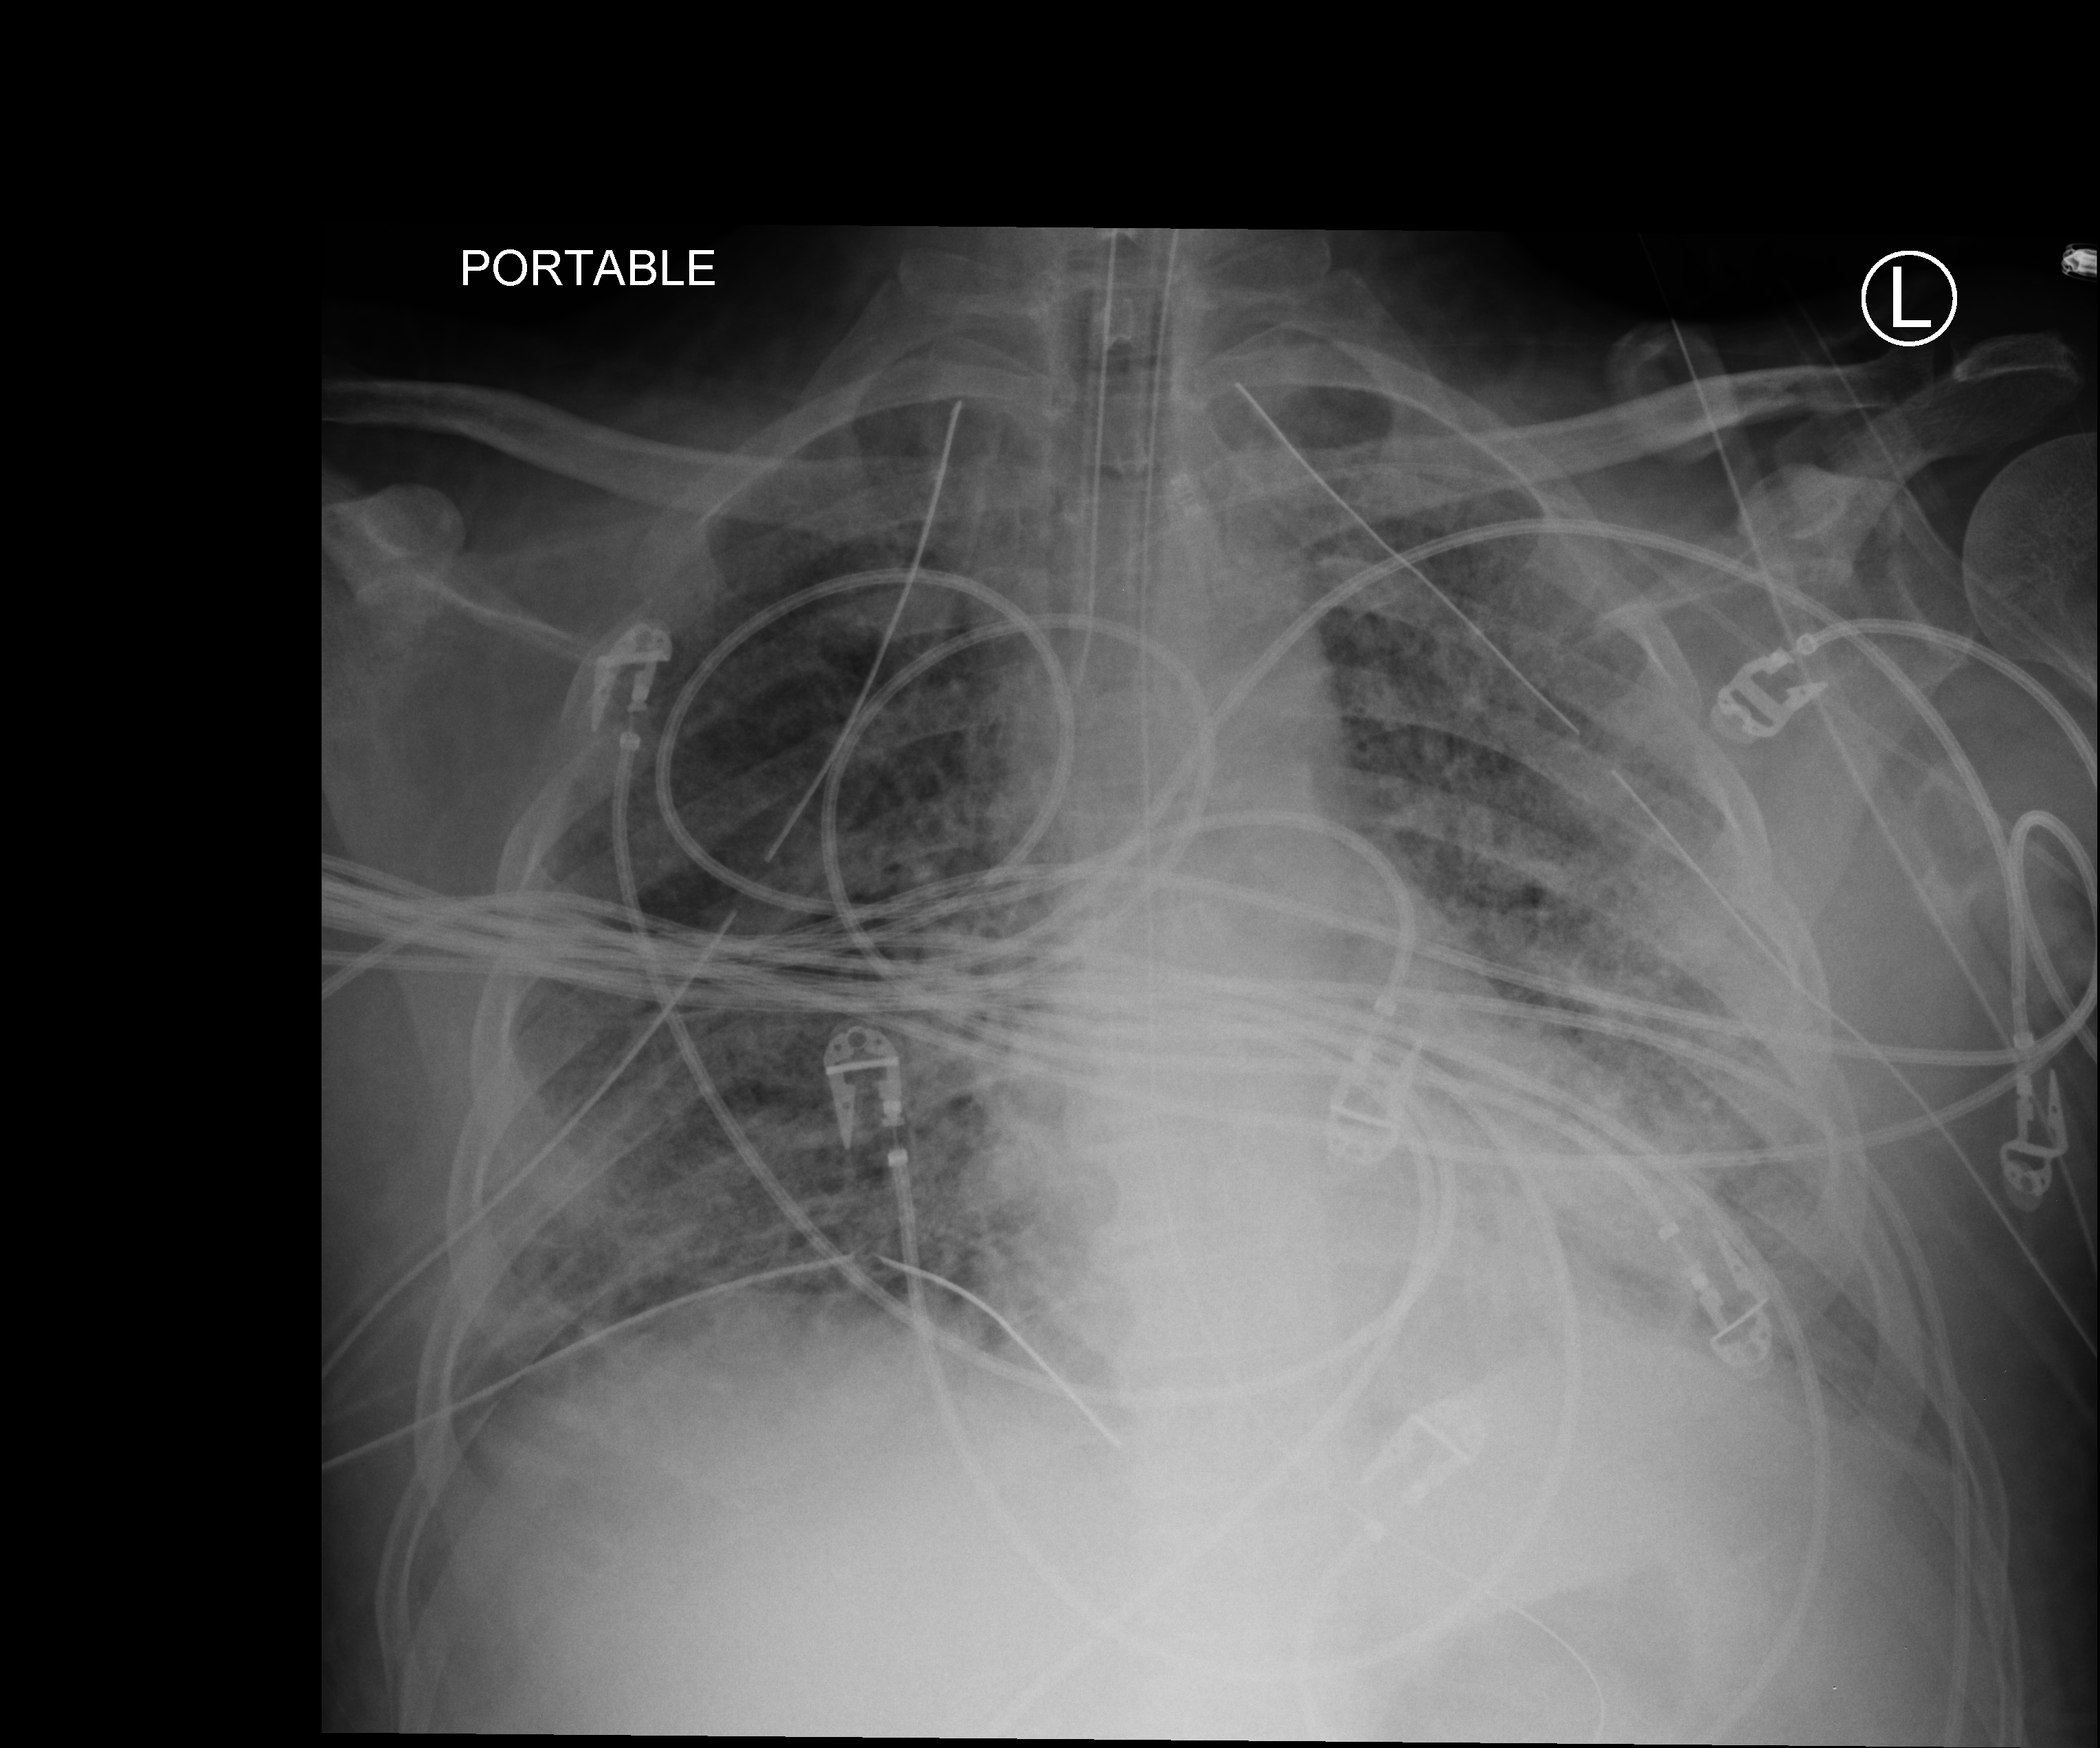
Chest X-ray (portable), anteroposterior (AP) projection. Male patient hospitalised with COVID-19, age 18–59 years.
From the hospital-stay record, not from the radiograph (when in the stay this image was taken is not recorded):
- admitted to intensive care during this hospital stay: yes
- mechanically ventilated during this hospital stay: yes
- length of hospital stay: 83 days